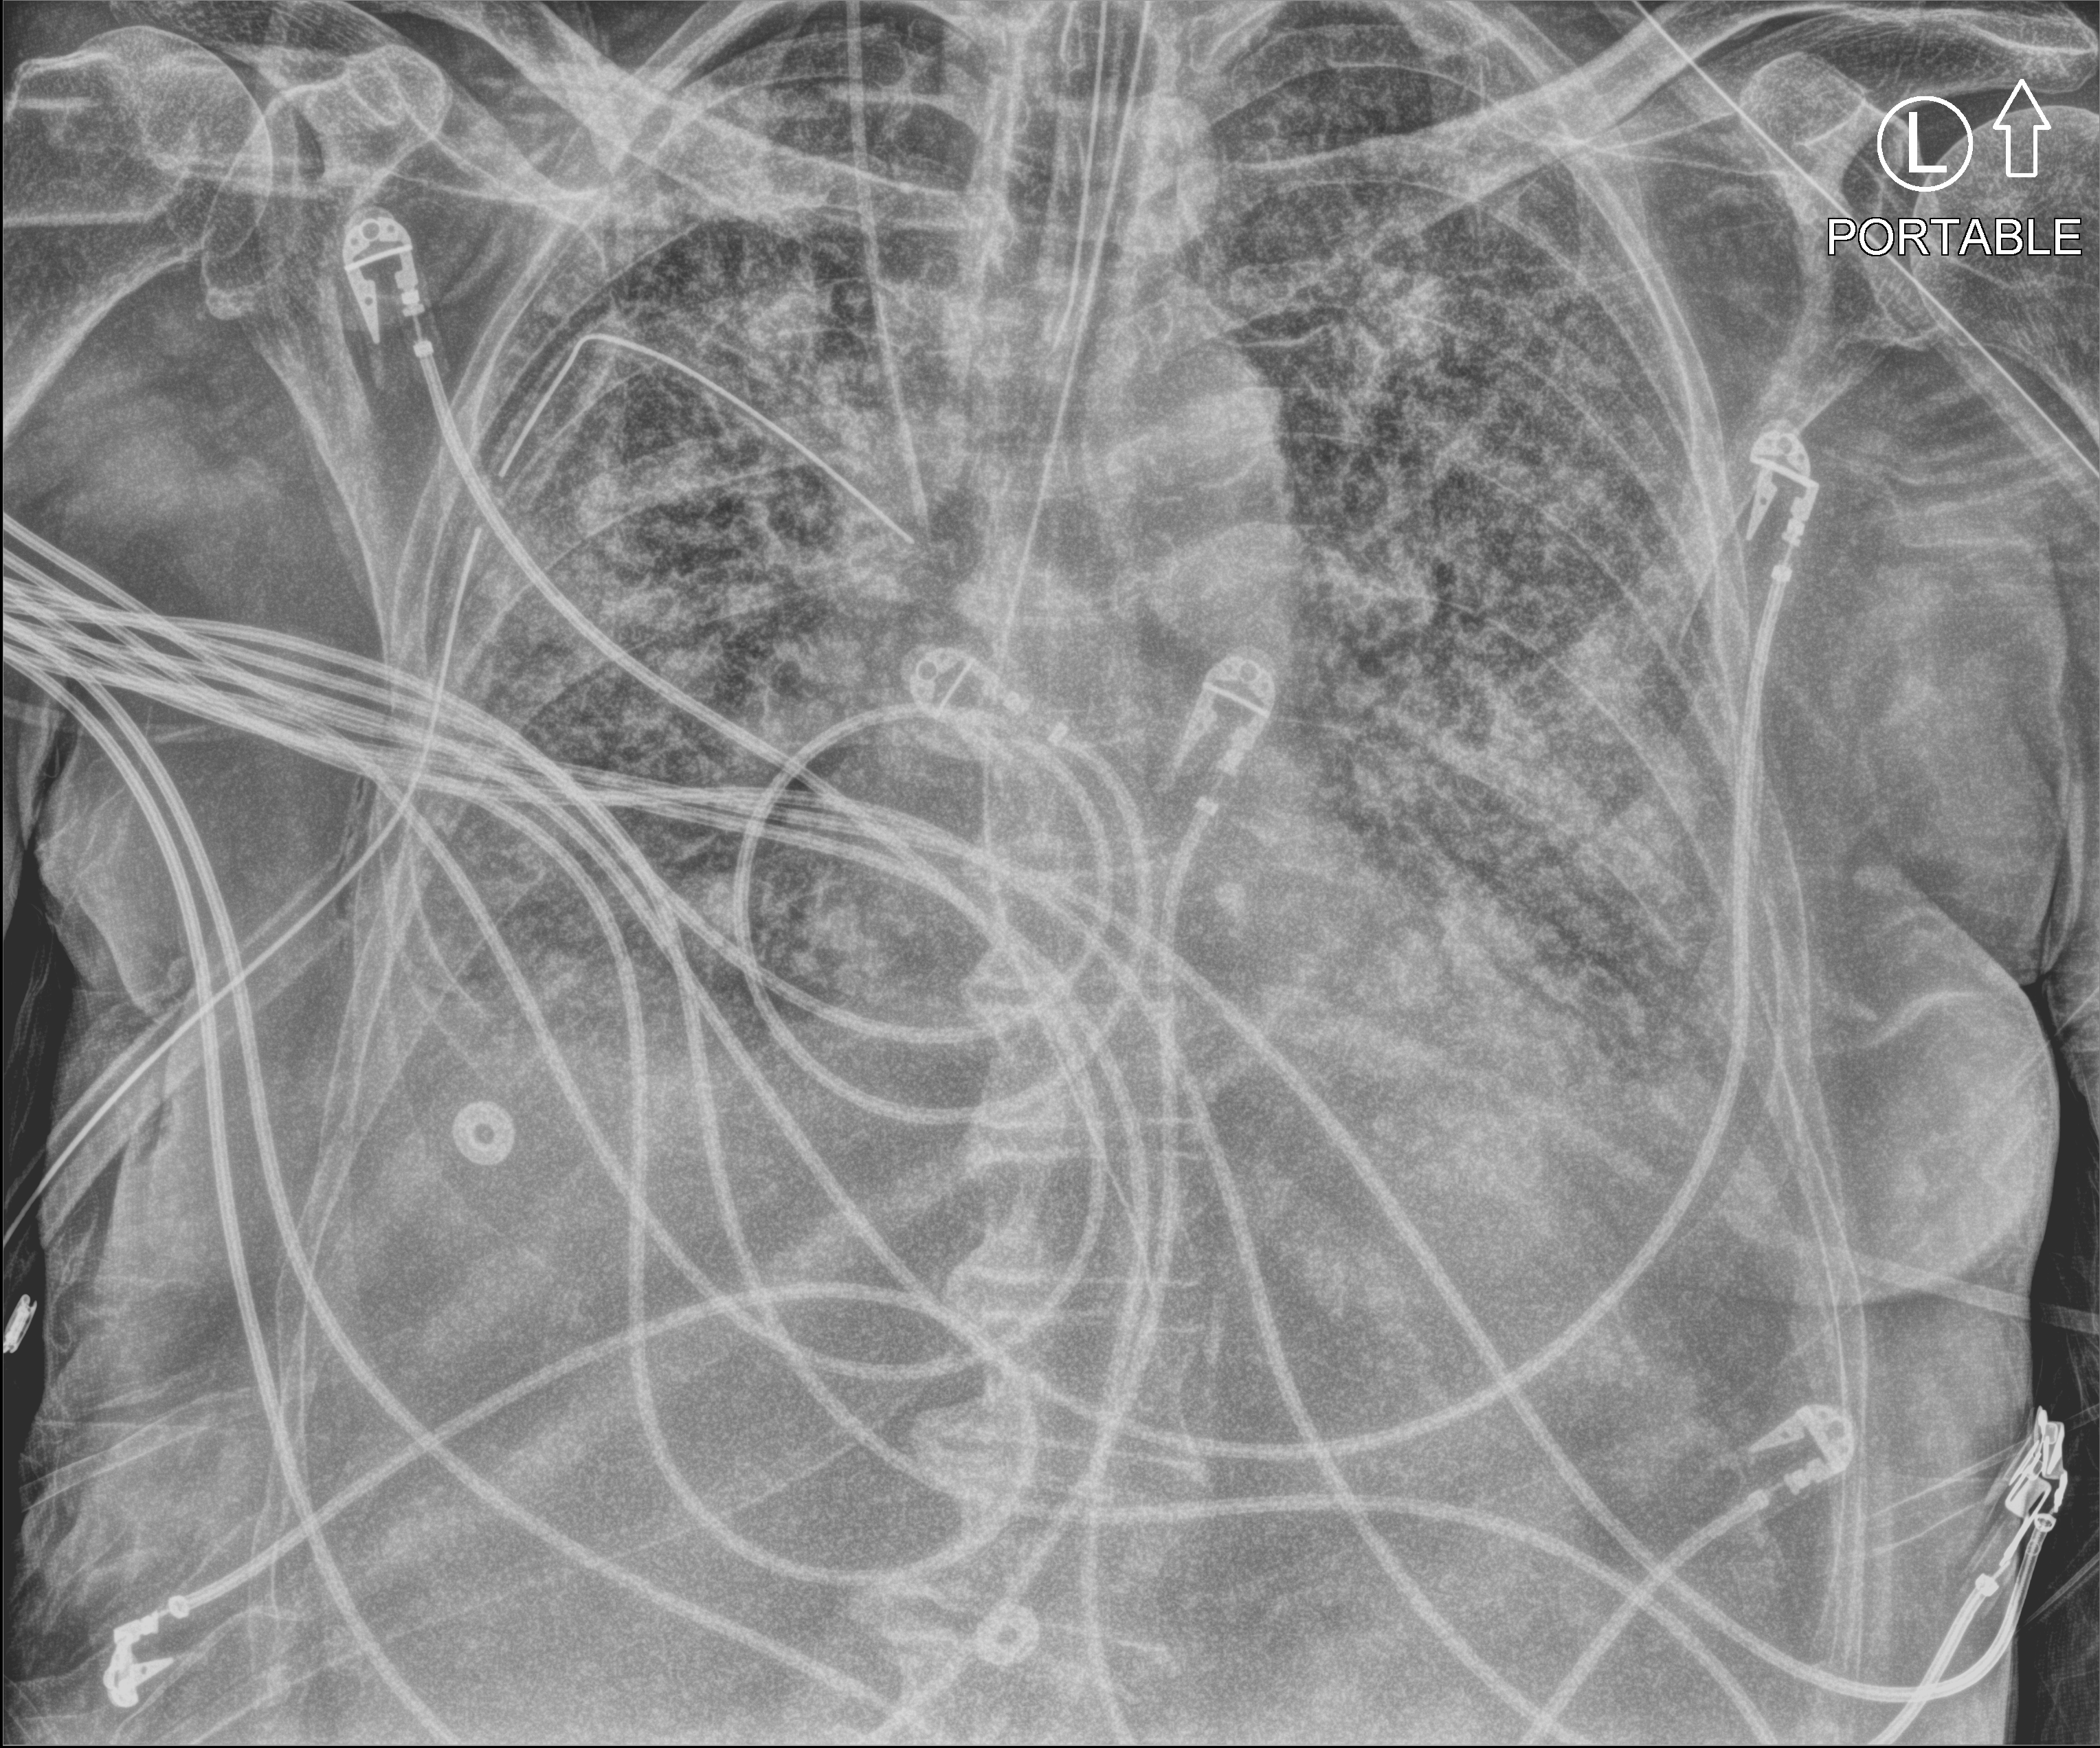
Bedside chest radiograph (computed radiography), anteroposterior (AP) projection. Patient hospitalised with COVID-19; male, aged 75–90 years.
Hospital-stay facts (about this admission, not read from this image; timing relative to this image not recorded): admitted to intensive care during this hospital stay: yes.